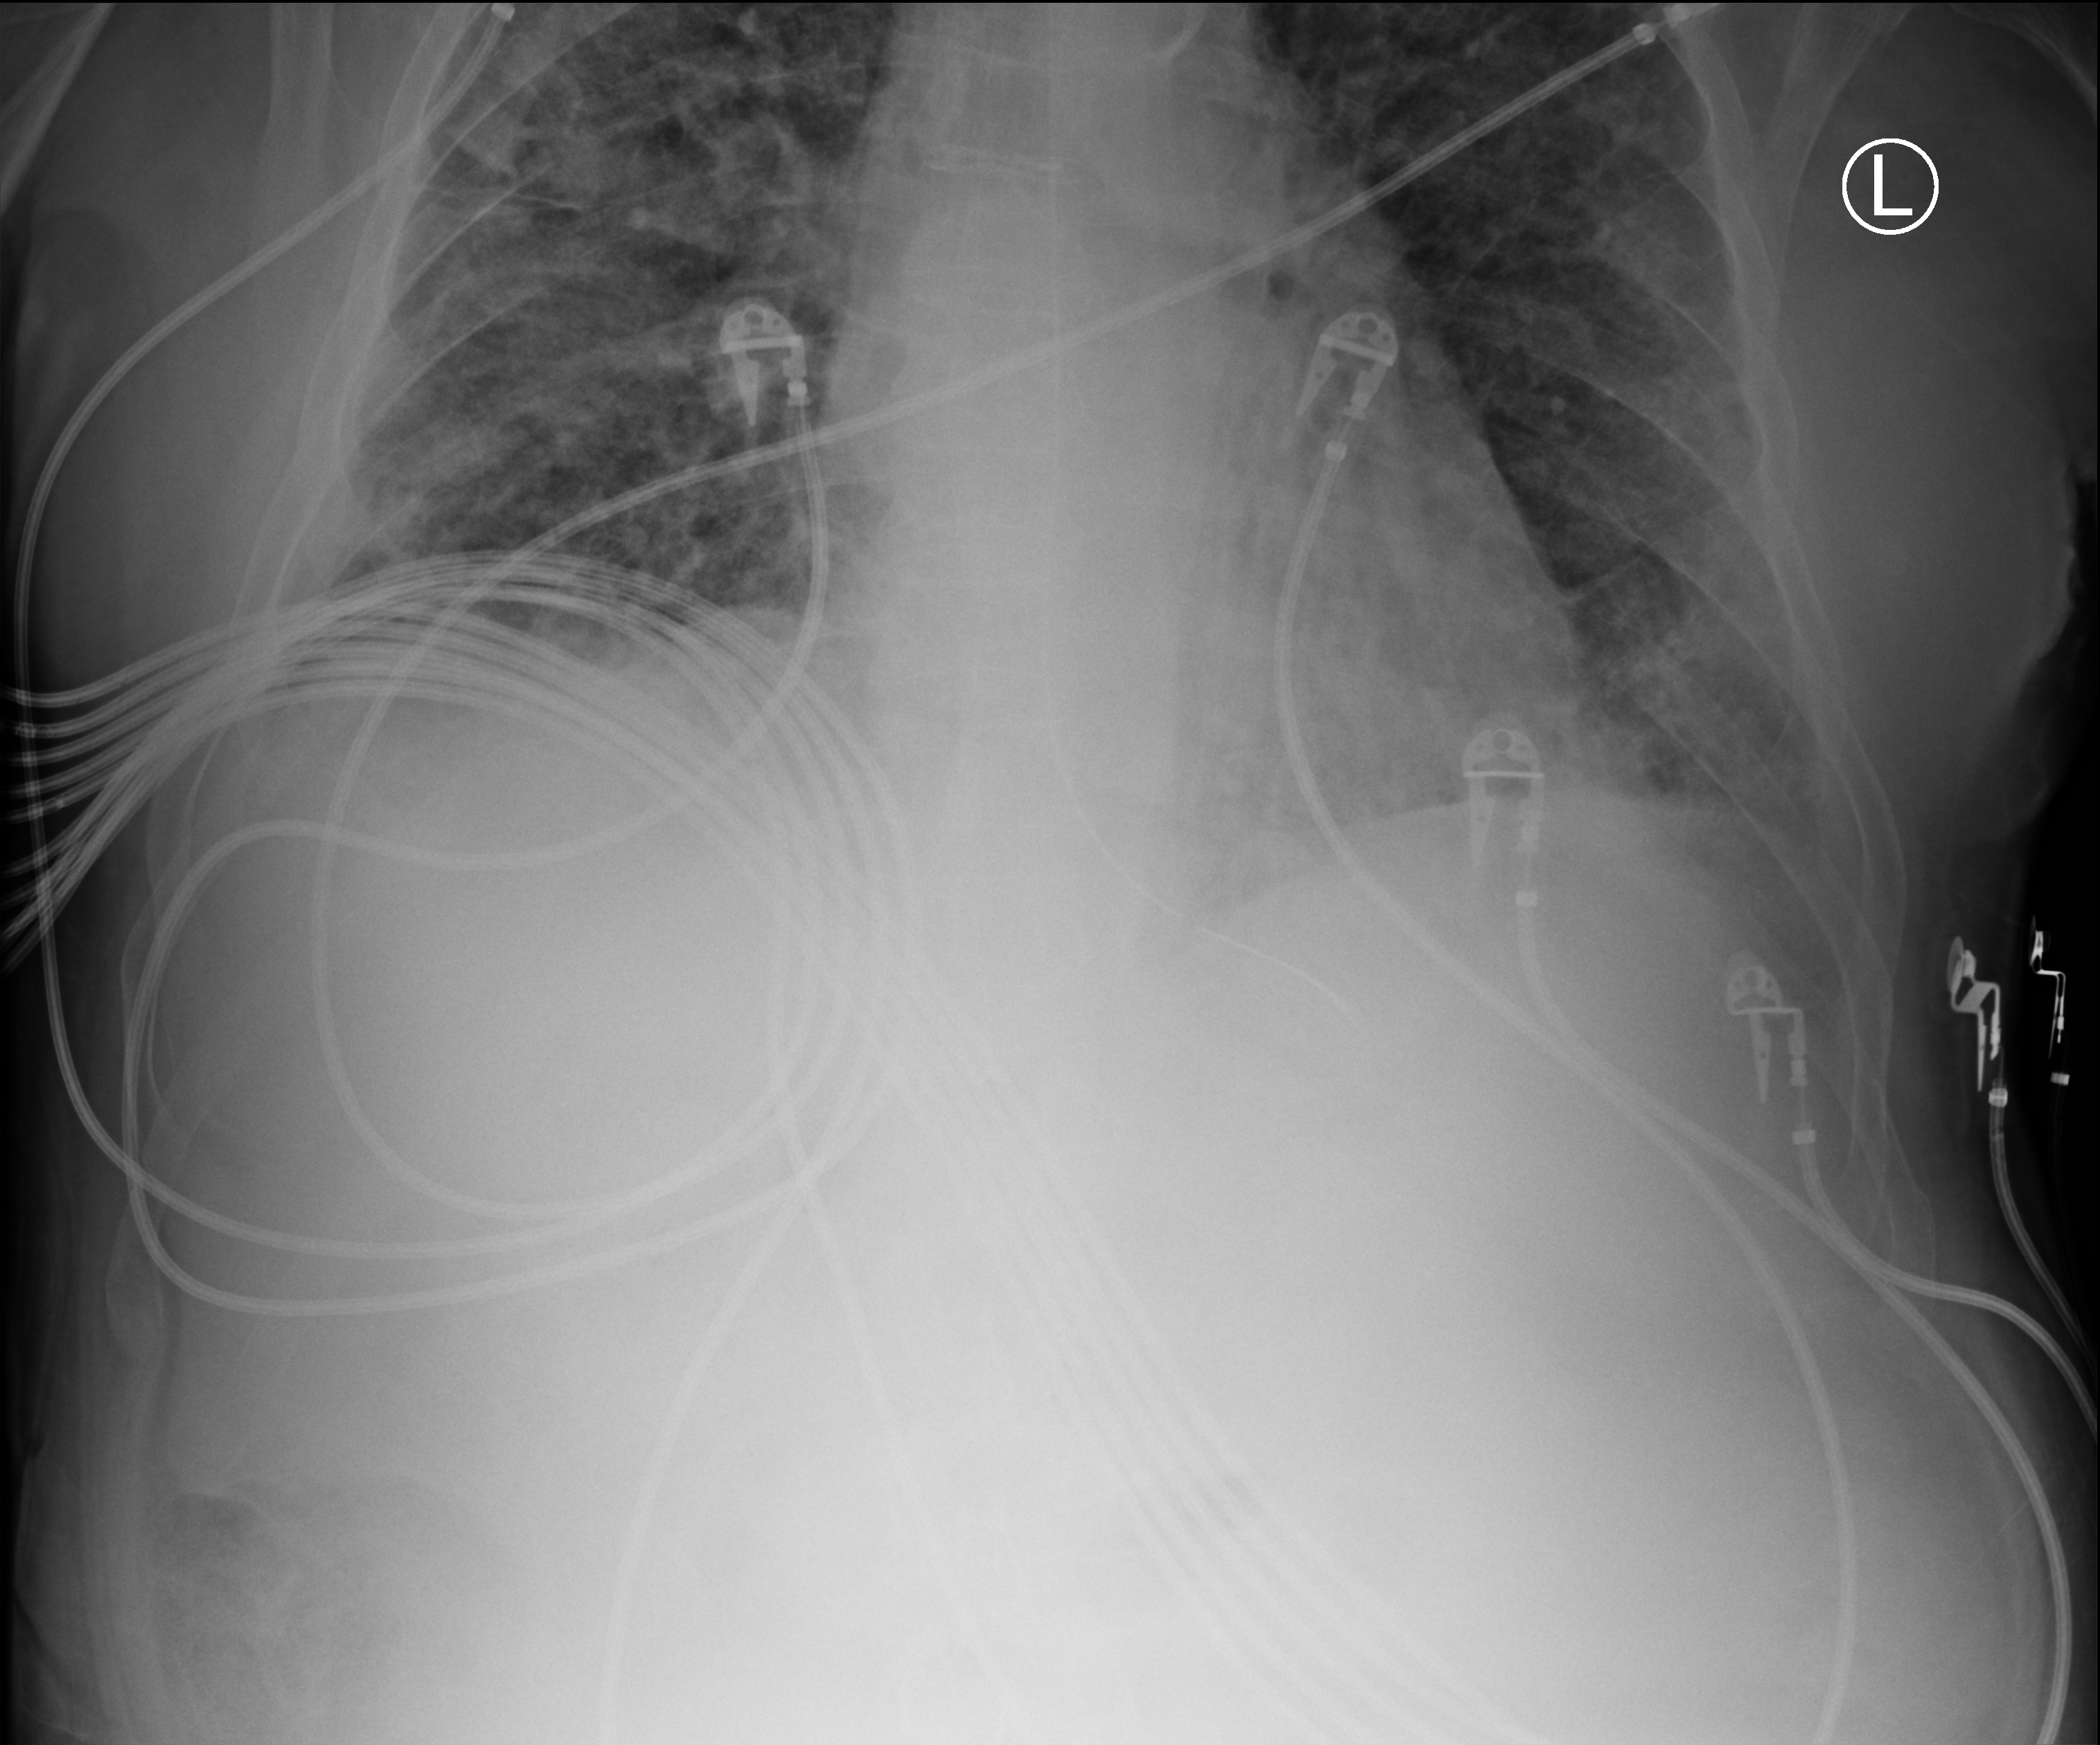
Portable chest radiograph, anteroposterior (AP) projection. Male patient hospitalised with COVID-19, age 60–74 years.
Admission-level facts for this patient (not findings on this image; timing relative to this image not recorded): mechanically ventilated during this hospital stay: yes.